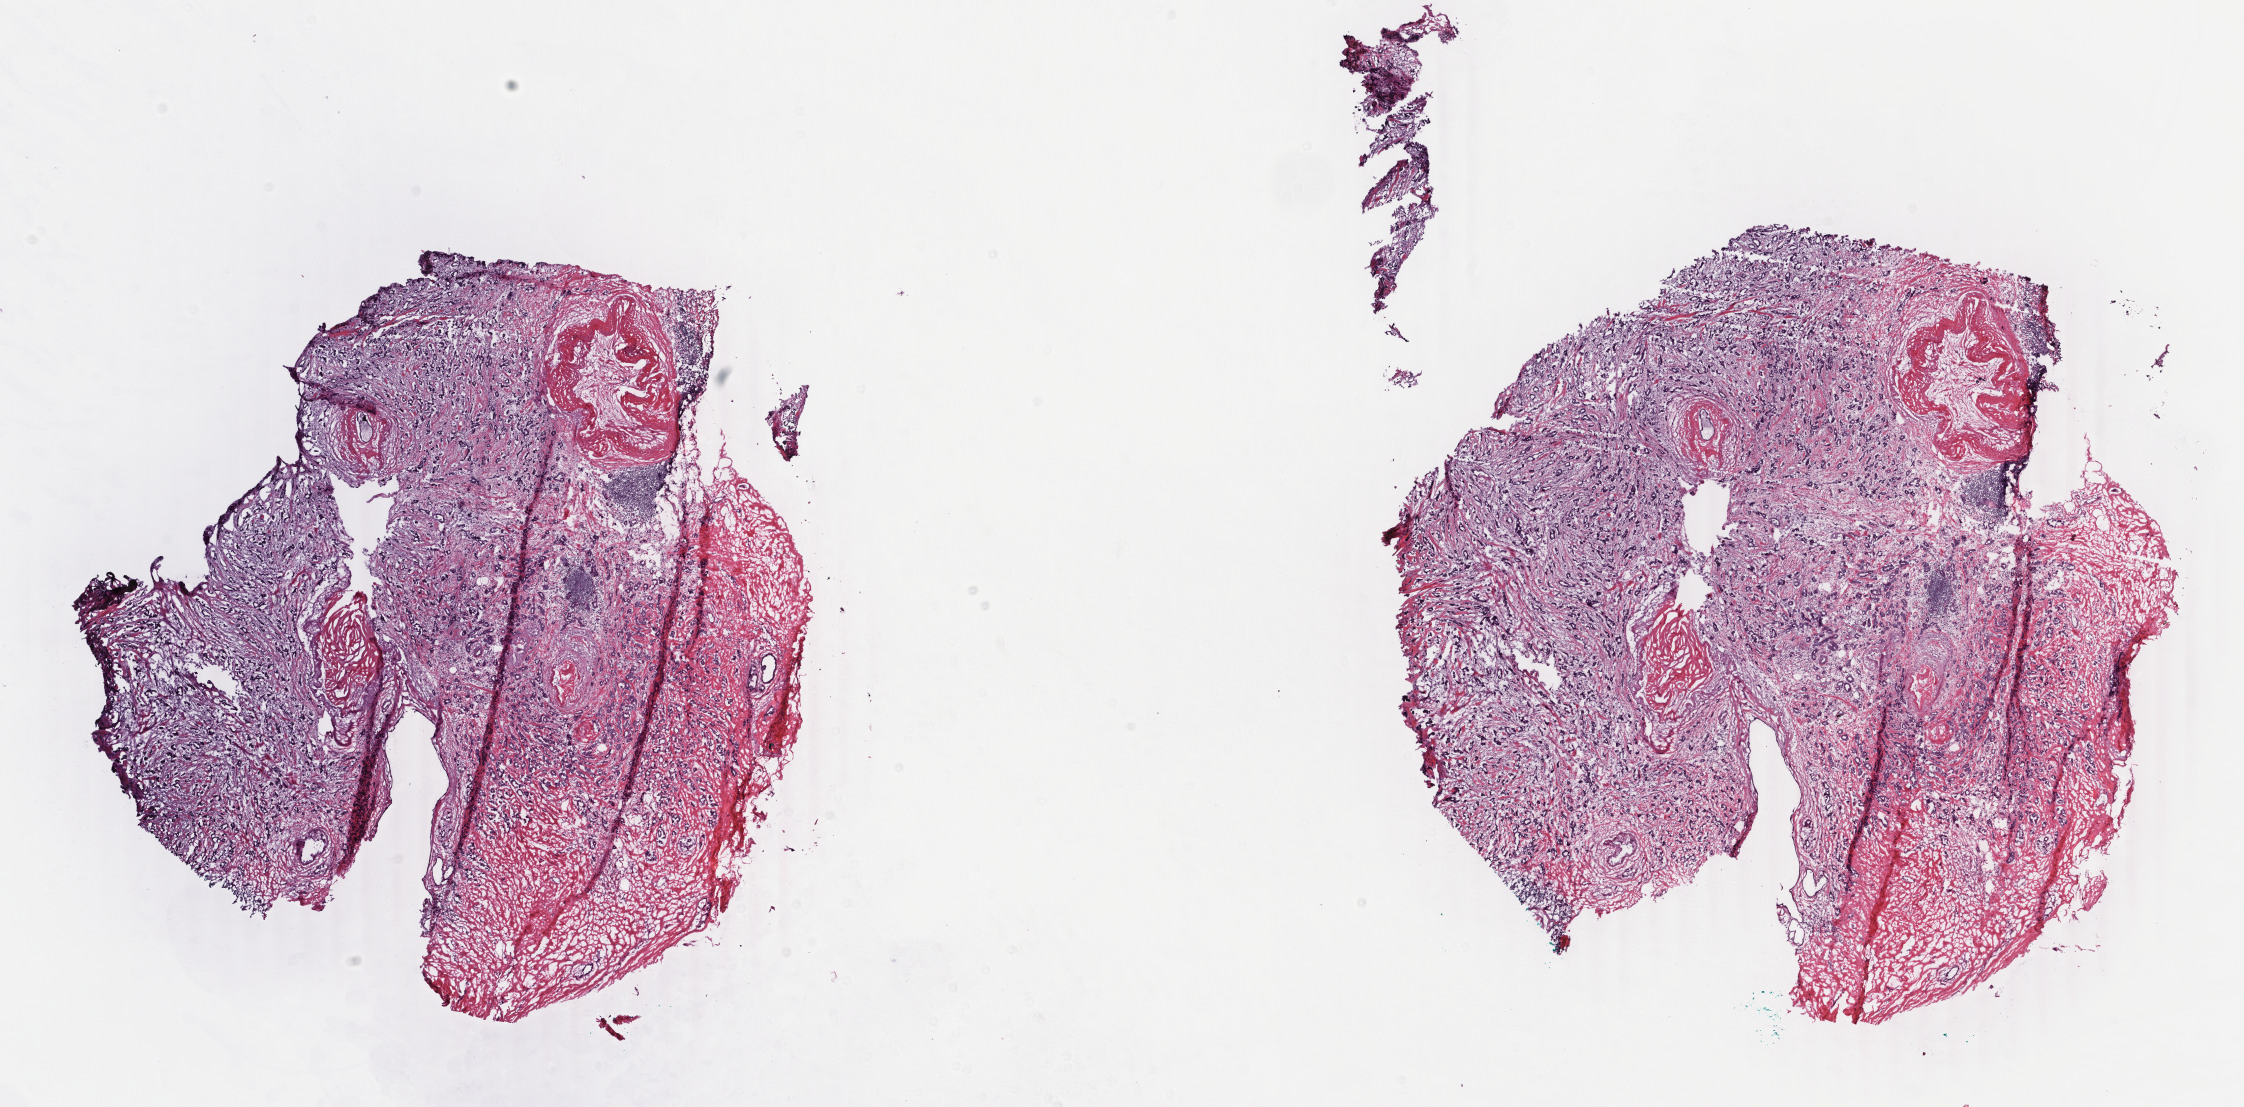
Digitized Hematoxylin and eosin (H&E) stained tissue section (whole slide), whole scanned area (about 17.8 x 8.8 mm, from a 40x scan) shown as a low-resolution overview. Frozen section. Sample: primary tumour, breast. Female patient; age at initial diagnosis 66 years. Composition of this section per pathologist review: tumour cells 75%, tumour nuclei 60%, normal cells 9%, stromal cells 10%, necrosis 1%. Infiltration values recorded for this section: lymphocyte infiltration 20%, monocyte infiltration 0%, neutrophil infiltration 0%.
AJCC pathologic stage: IA (5th edition). Laterality: right. Histologic diagnosis: Infiltrating duct carcinoma, NOS.